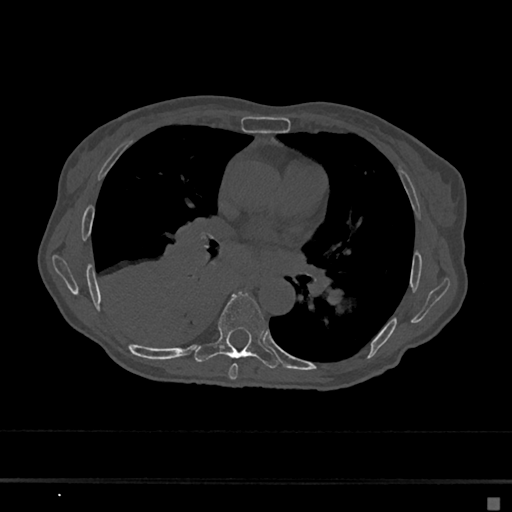
CT including the spine, one axial slice; slice 382 of 797 in the series (ordered by position); bone window (W 1800 / L 400 HU); 0.5 mm slice thickness; 512 × 512 image matrix, field of view 360 × 360 mm. Female patient, age 68 years. From the clinical record (not read from this slice): primary cancer: renal.
Outlined on this slice (semi-automatic segmentation, software-assisted and operator-edited):
- T6 vertebra: bounding box <228,363,238,380> (left, top, right, bottom; pixels)
- T7 vertebra: <195,292,279,369>